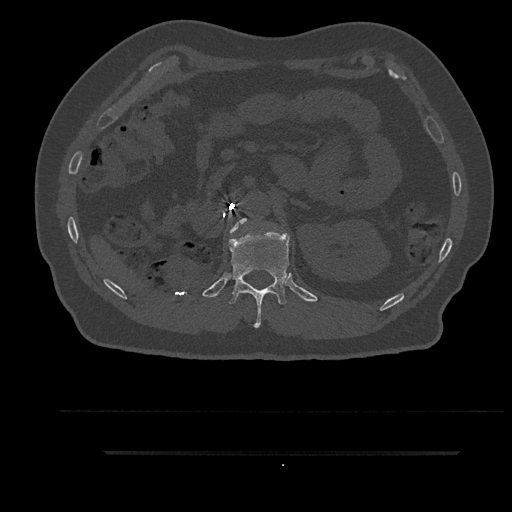
CT including the spine, one axial slice. Slice 233 of 797 in the series (ordered by position). Reconstruction kernel Br40s/3. Bone window (W 1800 / L 400 HU). 0.5 mm slice thickness. 512 × 512 image matrix, field of view 432 × 432 mm. Male patient, age 63 years. From the clinical record (not read from this slice): primary cancer: renal.
Structures marked on this image (semi-automatic segmentation, software-assisted and operator-edited):
- L1 vertebra: bounding box (x1, y1, x2, y2) in pixels: (230, 219, 247, 233)
- T12 vertebra: (229, 230, 289, 328)